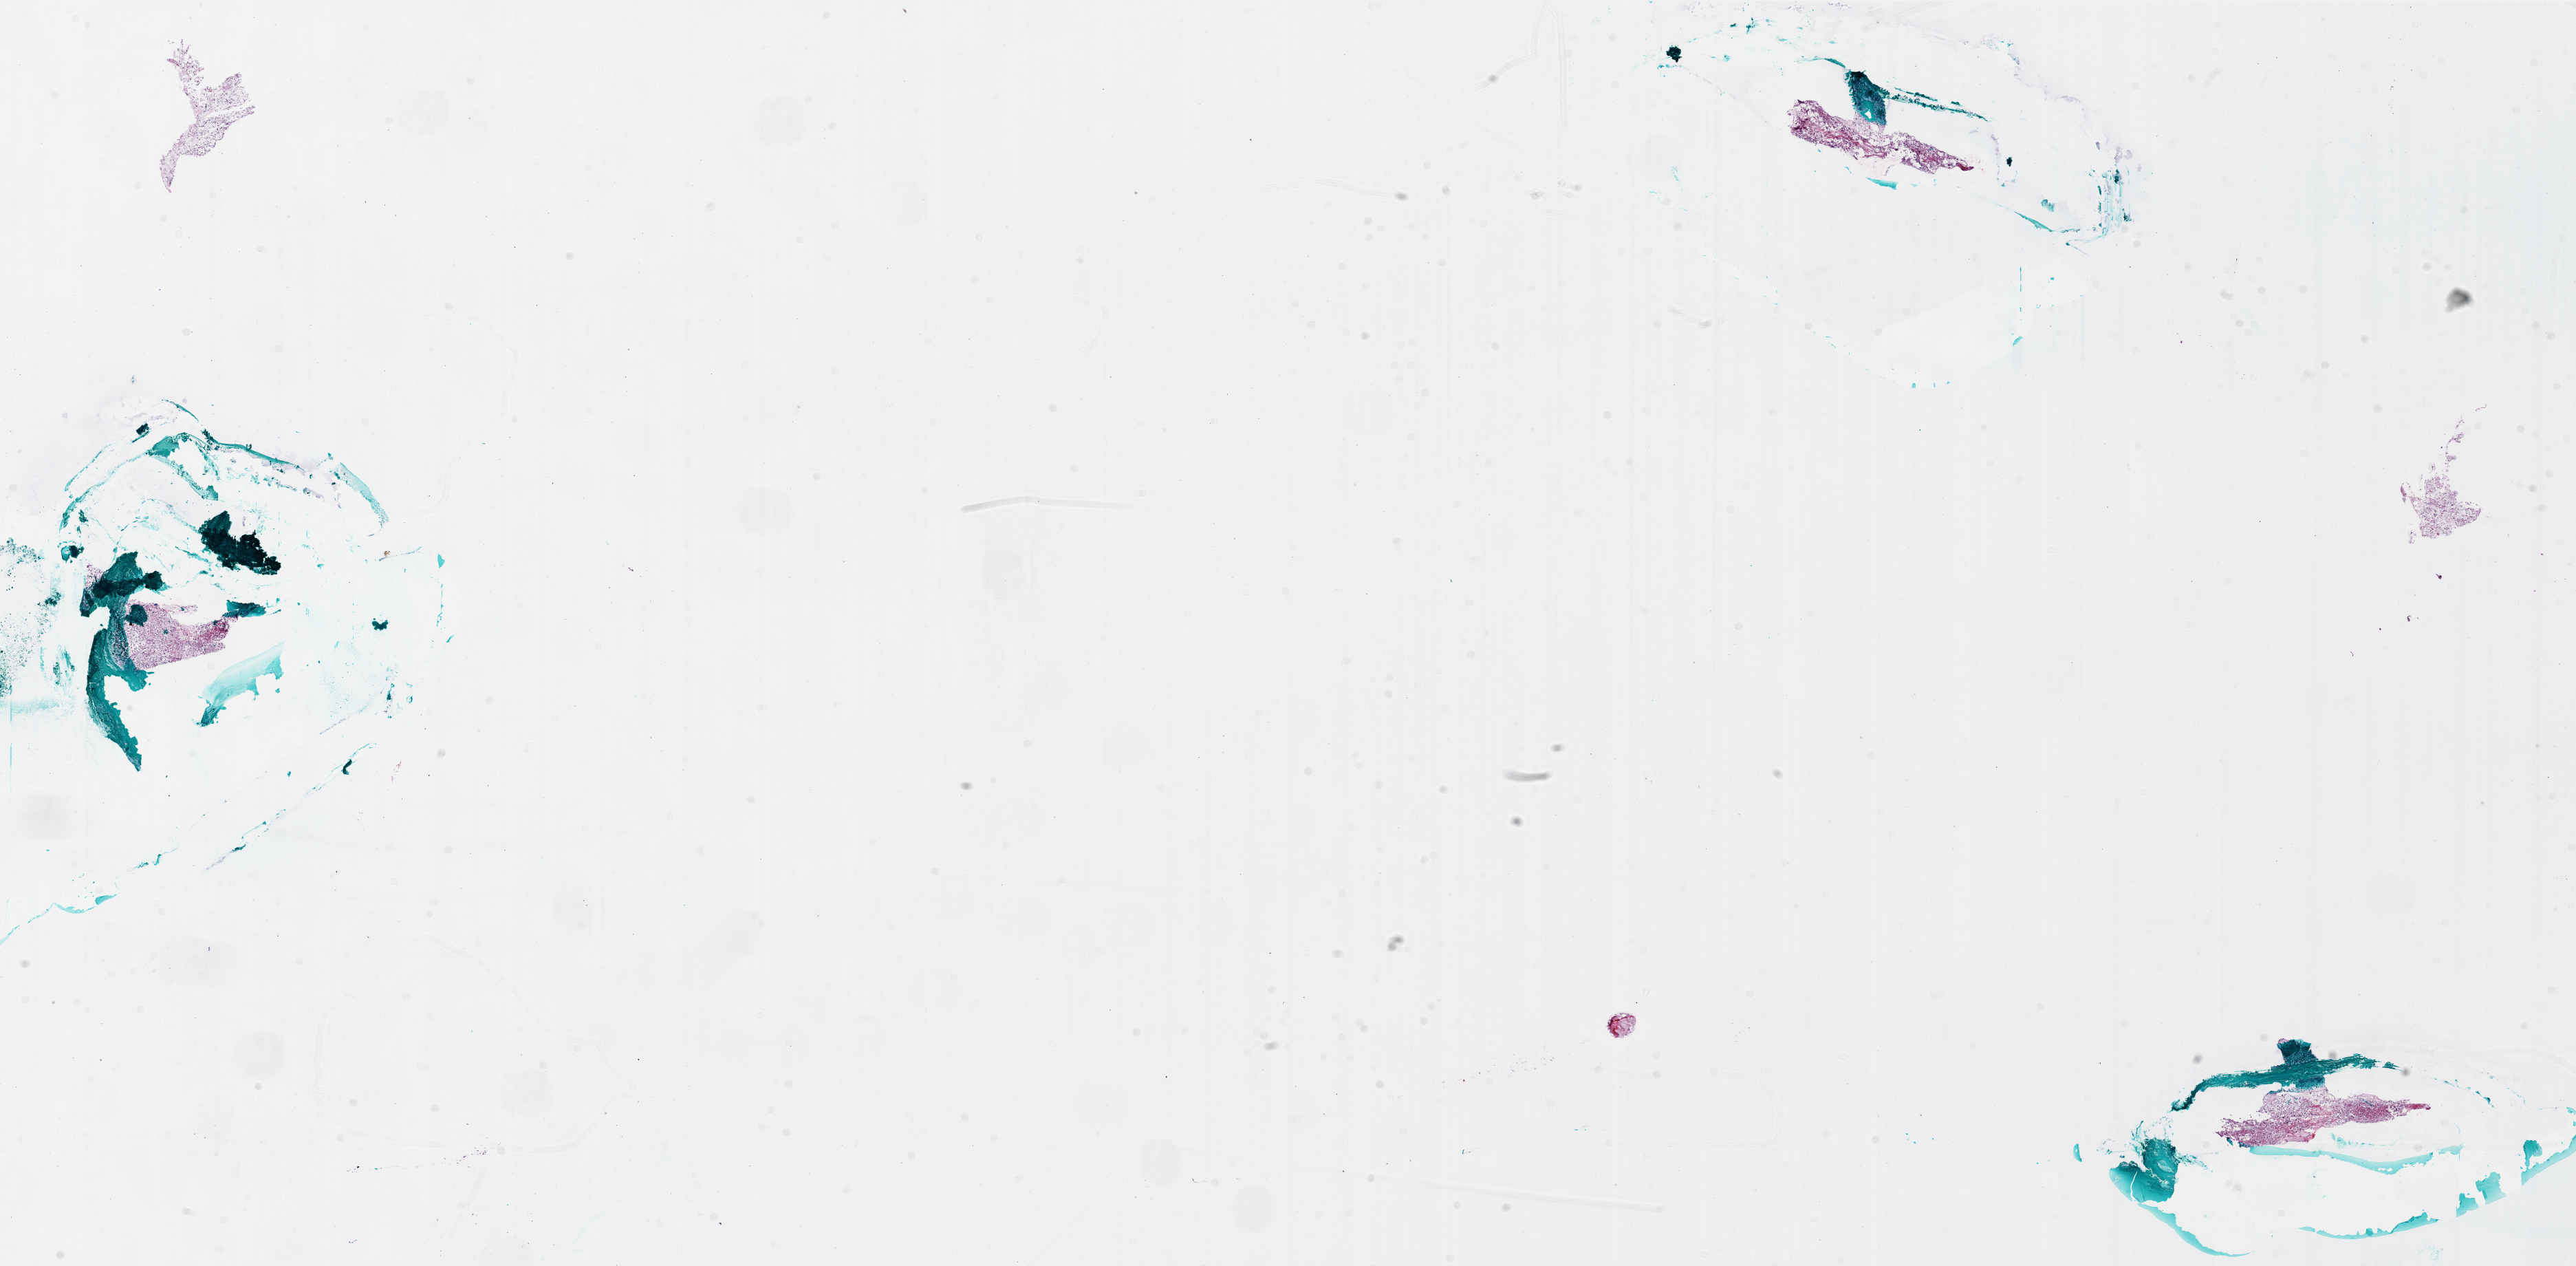
Whole-slide histology image, H&E-stained — a low-resolution overview of the entire scanned area, about 30.0 x 14.7 mm; frozen section from the bottom of the tissue portion; brain, primary tumour sample. Patient: male, age at initial diagnosis 25 years.
Pathologic diagnosis: Glioblastoma.